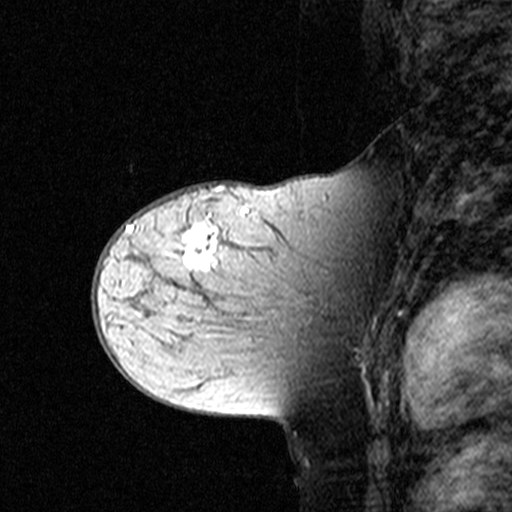
Breast MRI (dynamic contrast-enhanced), one sagittal slice. Position 24 of 44 along the scan axis. Dynamic contrast-enhanced study with each time point stored as its own series, time point 2 of 3 at this slice position (early post-contrast, ordered by acquisition time). 1.5 T. TE 4.5 ms, TR 11 ms. 3 mm slice thickness. 512 × 512 image matrix, field of view 200 × 200 mm. Female patient, age 44 years. Case-level facts recorded for this patient, not image findings: setting: breast cancer imaged before/during neoadjuvant chemotherapy; receptor status: triple-negative.
Structures marked on this image (semi-automatic segmentation, software-assisted and operator-edited):
- analysis volume of interest (the breast-tissue region the enhancement analysis was run in; not a lesion): bounding box [x1, y1, x2, y2] px = [142, 208, 349, 363]
- tumour enhancement mask (voxels above the 90 % enhancement threshold inside the analysis volume of interest): [184, 210, 247, 269]